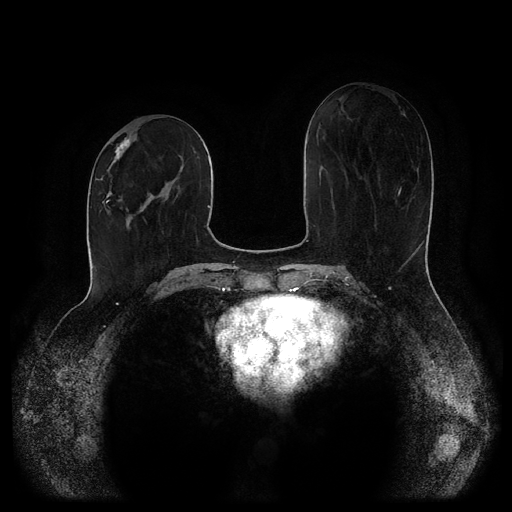
Breast MRI (dynamic contrast-enhanced, multi-phase), one axial slice; slice 42 of 116 in the series (ordered by position); dynamic contrast-enhanced series, time point 2 of 5 at this slice position (early post-contrast); 1.5 T; TE 2.6 ms, TR 5.2 ms; 2 mm slice thickness; 512 × 512 image matrix, field of view 380 × 380 mm. Female patient, age 52 years.
Outlined on this slice (semi-automatically segmented with operator editing):
- breast lesion (labelled 'tumour' in the annotation; benign lesions carry a separate 'benign' label): bounding box (x1, y1, x2, y2) in pixels: (97, 134, 131, 180)